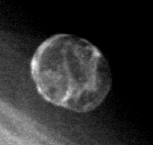
Region of interest cut from a scanned film mammogram (one marked finding), left breast, CC view.
Calcifications, morphology eggshell; BI-RADS assessment category 2; subtlety rating 5 on a 1 (subtle) to 5 (obvious) scale; benign; no additional work-up was recommended (benign without callback).